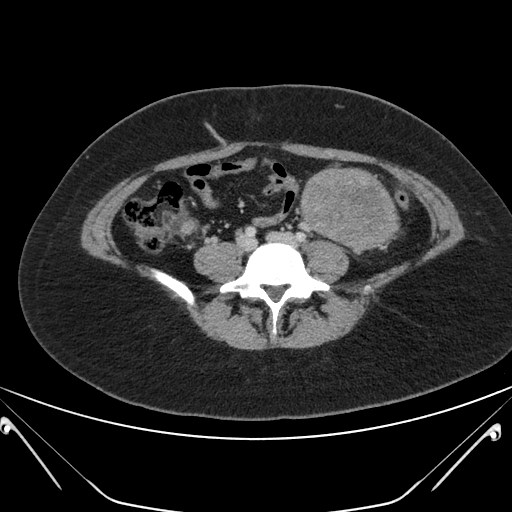
Contrast-enhanced abdominal CT, one axial slice. Position 70 of 168 along the scan axis. 120 kVp. Intravenous contrast given. Soft-tissue window (W 400 / L 40 HU). 3 mm slice thickness. 512 × 512 image matrix. Patient: female, 26 years. Case-level facts recorded for this patient, not image findings: diagnosis: adrenocortical carcinoma; tumour side: left adrenal.
Structures marked on this image (semi-automatically segmented with operator editing):
- mass: box from (x=301, y=169) to (x=395, y=250) px